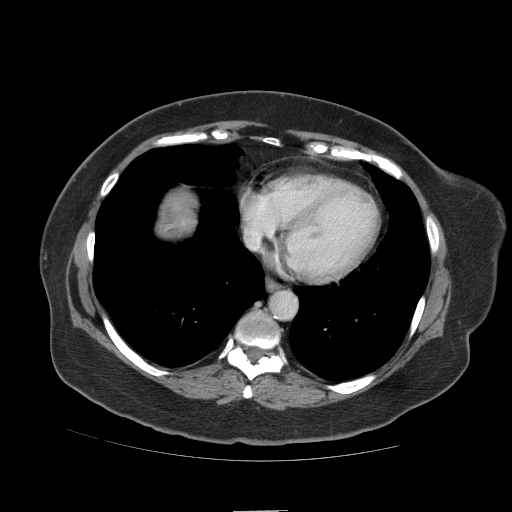
Contrast-enhanced abdominal CT (liver protocol), one axial slice. Position 103 of 109 along the scan axis. Reconstruction kernel STANDARD. Soft-tissue window (W 400 / L 40 HU). 2.5 mm slice thickness. 512 × 512 image matrix, field of view 420 × 420 mm. From the clinical record (not read from this slice): diagnosis: hepatocellular carcinoma (patient treated with transarterial chemoembolisation; whether this scan precedes or follows treatment is not stated here); TNM stage (as recorded): Stage-IVB; Child-Pugh class: A; tumour differentiation: poorly differentiated; tumour nodularity: multinodular.
Structures marked on this image (semi-automatically segmented with operator editing):
- liver parenchyma outside the tumour (the mass and vessels are separate outlines, so this box may not span the whole liver): bounding box <158,190,196,236> (left, top, right, bottom; pixels)